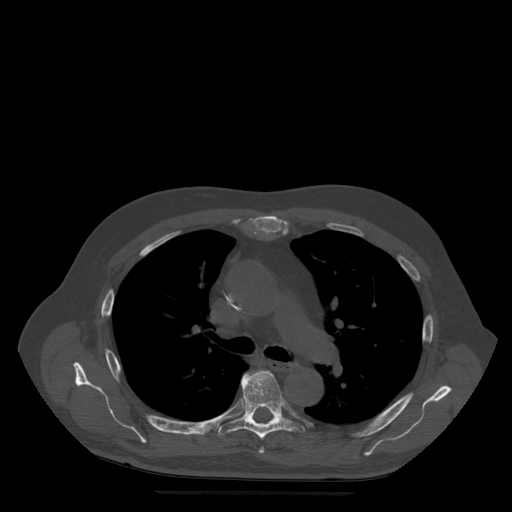
CT including the spine, one axial slice; slice 356 of 522 in the series (ordered by position); bone window (W 1800 / L 400 HU); 512 × 512 image matrix, field of view 420 × 420 mm. Patient age 72 years. Case-level facts recorded for this patient, not image findings: primary cancer: prostate.
Annotated regions visible in this slice (semi-automatic segmentation, software-assisted and operator-edited):
- T5 vertebra: bounding box [x1, y1, x2, y2] px = [259, 448, 265, 454]
- T6 vertebra: [219, 371, 305, 440]